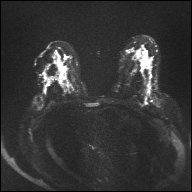
Breast MRI, one axial slice. Slice 20 of 32 in the series (ordered by position). Diffusion-weighted series; image 2 of 4 stored at this slice position (different b-values; order by instance number). 1.5 T. 192 × 192 image matrix. Female patient.
Structures marked on this image (manually delineated by an expert):
- tumour on diffusion-weighted imaging: box from (x=147, y=88) to (x=151, y=94) px